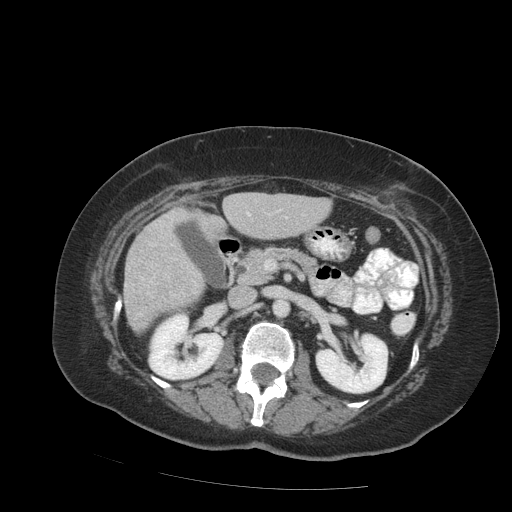
Contrast-enhanced abdominal CT (liver protocol), one axial slice. Slice 36 of 99 in the series (ordered by position). Soft-tissue window (W 400 / L 40 HU). 512 × 512 image matrix, field of view 400 × 400 mm. From the clinical record (not read from this slice): diagnosis: hepatocellular carcinoma (patient treated with transarterial chemoembolisation; whether this scan precedes or follows treatment is not stated here); TNM stage (as recorded): Stage-IVB; Child-Pugh class: A.
Outlined on this slice (semi-automatic segmentation, software-assisted and operator-edited):
- liver parenchyma outside the tumour (the mass and vessels are separate outlines, so this box may not span the whole liver): bounding box <124,192,330,332> (left, top, right, bottom; pixels)
- liver vessels: <142,210,287,279>